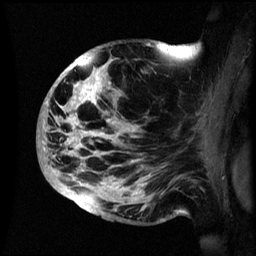
Breast MRI (dynamic contrast-enhanced), one sagittal slice. Position 35 of 60 along the scan axis. Dynamic contrast-enhanced series, image 2 of 3 at this slice position (ordered by acquisition). 1.5 T. TE 4.2 ms, TR 8.4 ms. 2.4 mm slice thickness. 256 × 256 image matrix, field of view 230 × 230 mm. Patient: female, 48 years.
Structures marked on this image (semi-automatic segmentation, software-assisted and operator-edited):
- analysis volume of interest (the breast-tissue region the enhancement analysis was run in; not a lesion): box from (x=38, y=41) to (x=195, y=222) px
- tumour enhancement mask (voxels above the 70 % enhancement threshold inside the analysis volume of interest): (x=42, y=56)–(x=134, y=212)